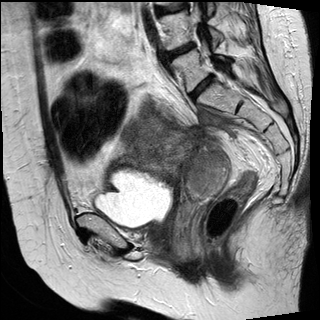
Pelvic MRI for cervical cancer, one sagittal slice. Slice 13 of 30 in the series (ordered by position). T2-weighted. 1.5 T. TE 89 ms, TR 3810 ms. 4 mm slice thickness. 320 × 320 image matrix. Female patient, age 62 years.
Structures marked on this image (manually delineated by an expert):
- uterus and cervix: box from (x=133, y=119) to (x=231, y=205) px